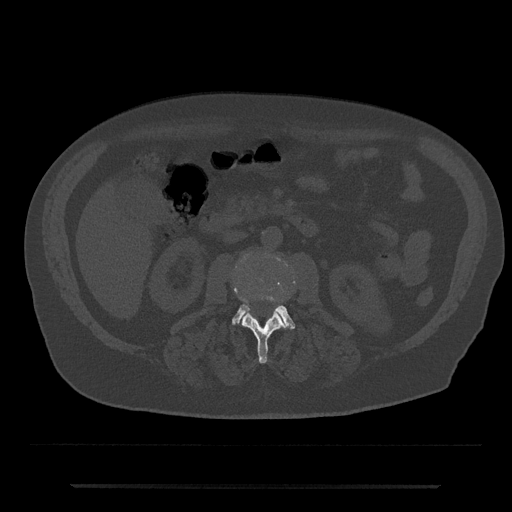
CT including the spine, one axial slice; position 445 of 797 along the scan axis; reconstruction kernel Br40s/3; 120 kVp; bone window (W 1800 / L 400 HU); 0.5 mm slice thickness; 512 × 512 image matrix, field of view 434 × 434 mm. Patient: male, 80 years. Case-level facts recorded for this patient, not image findings: primary cancer: prostate; vertebrae with lytic lesions (as recorded): L1, T11.
Structures marked on this image (semi-automatically segmented with operator editing):
- L2 vertebra: bounding box (x1, y1, x2, y2) in pixels: (235, 288, 288, 364)
- L3 vertebra: (232, 294, 295, 329)